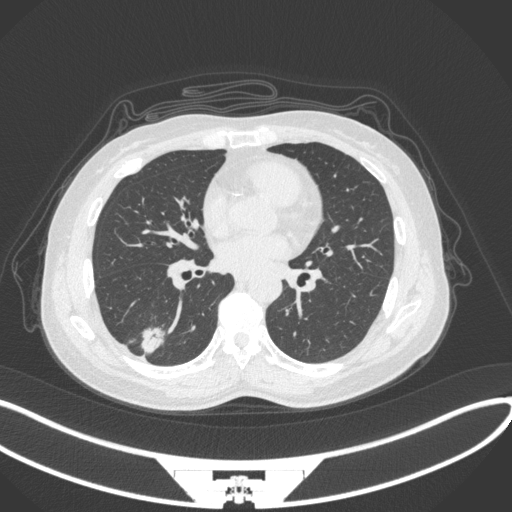
Chest CT, one axial slice. Slice 137 of 352 in the series (ordered by position). 120 kVp. Lung window (W 1500 / L -600 HU). 1 mm slice thickness. 512 × 512 image matrix, field of view 400 × 400 mm. Female patient, age 55 years. Case-level facts recorded for this patient, not image findings: clinical TNM (as recorded): T1c N1 M0.
Outlined on this slice (bounding box drawn by a radiologist):
- lung tumour (recorded histology: adenocarcinoma): bounding box (x1, y1, x2, y2) in pixels: (134, 323, 168, 356)